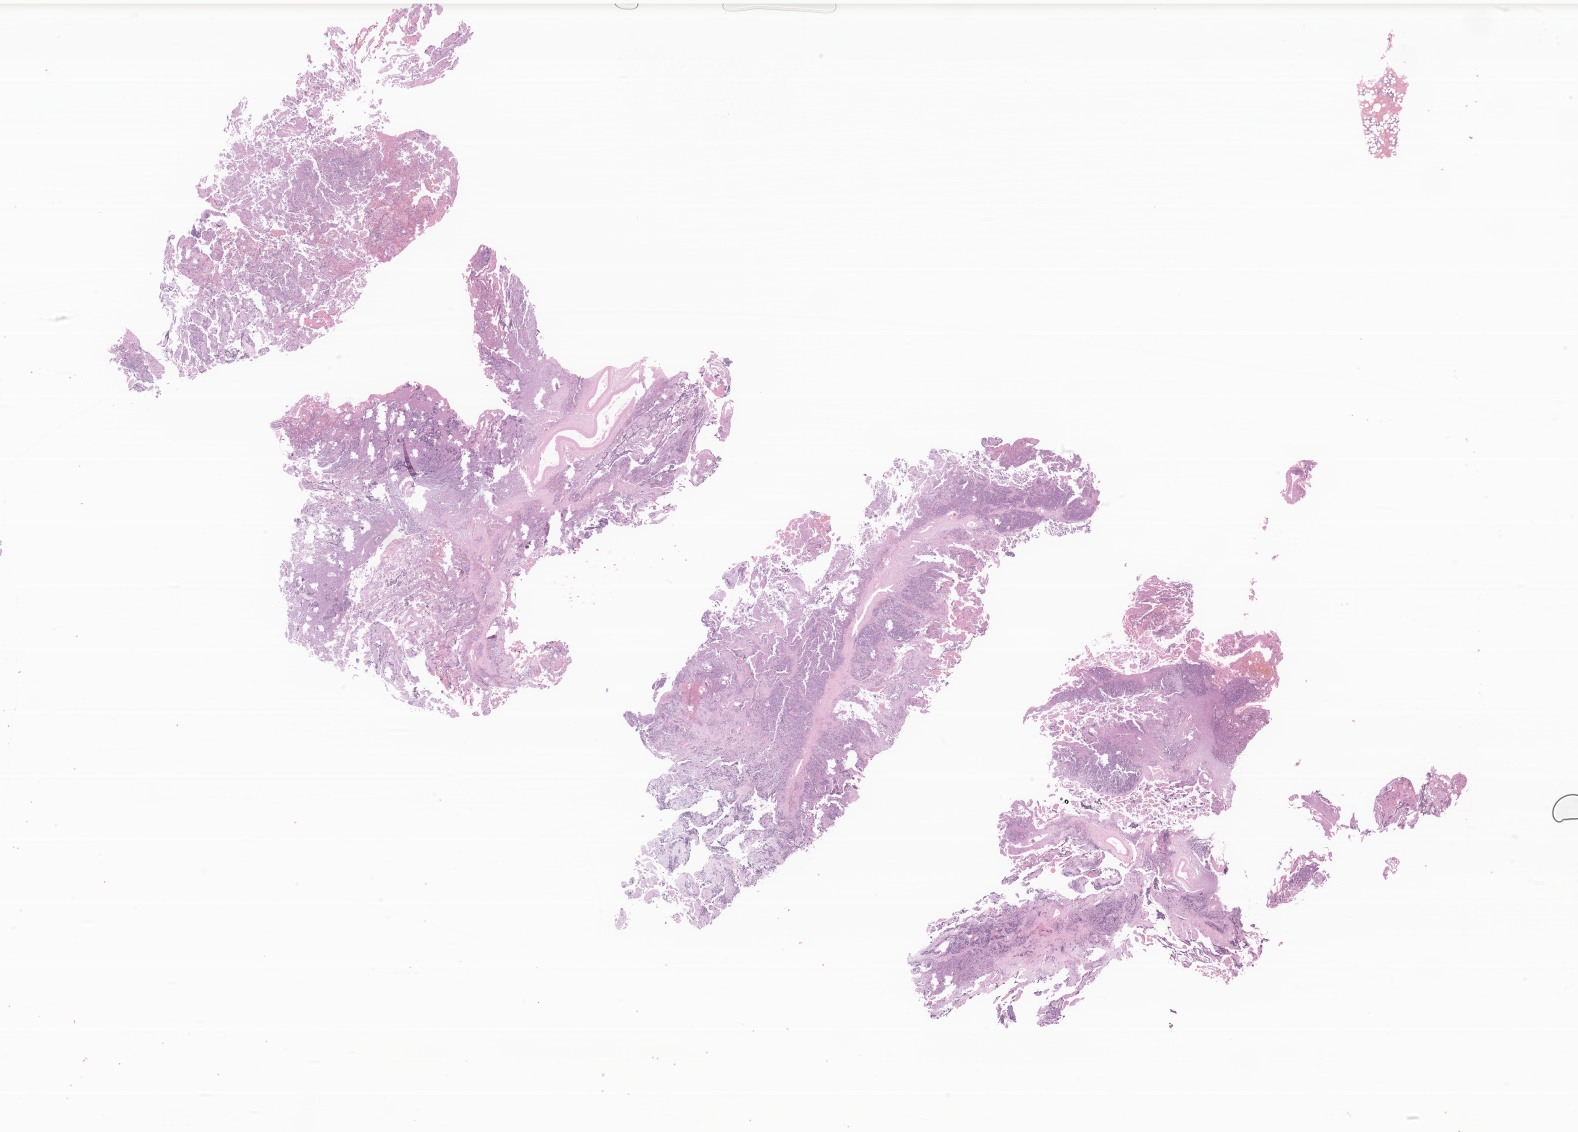
Digitized H&E-stained section of tumor tissue from the brain, a low-resolution overview of the entire scanned area, about 26.6 x 19.1 mm; FFPE section. Female patient, age 284 months (23 years 8 months).
Diagnosis (ICD-O-3 morphology term): Medulloblastoma, NOS.